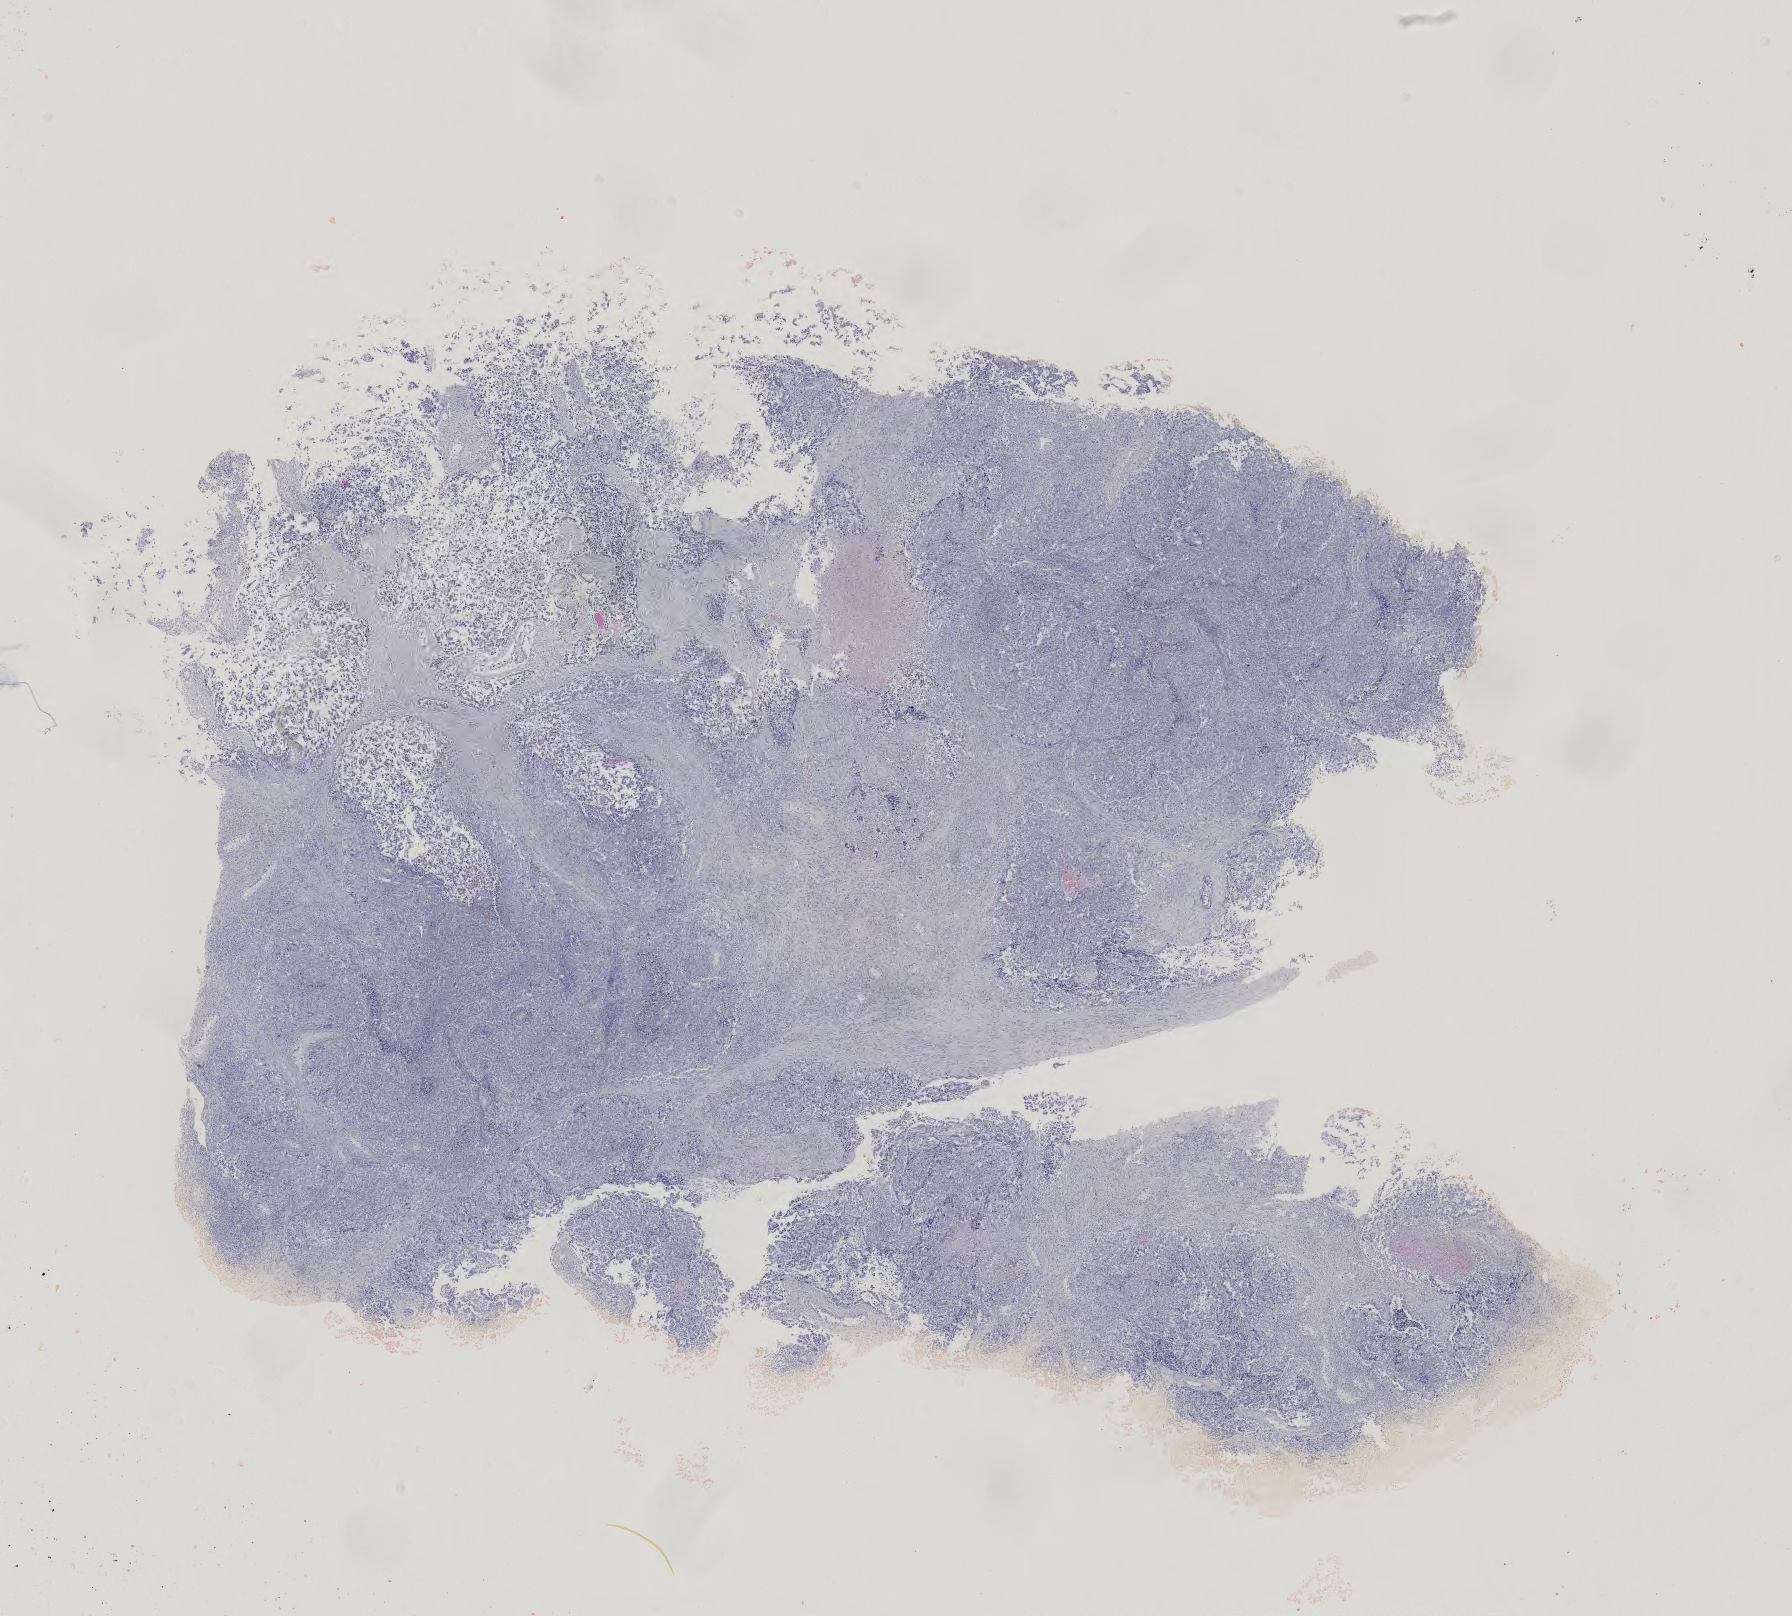
Whole-slide histology image, H&E, shown as a low-resolution overview of the whole scanned area (about 13.1 x 11.8 mm, acquisition: 40x scan). Formalin-fixed paraffin-embedded (FFPE) diagnostic section. Sample: primary tumour, testis. Patient: male, age at initial diagnosis 26 years.
Diagnosis: Embryonal carcinoma, NOS. AJCC pathologic stage: II (4th edition). TNM: T2 NX M0.